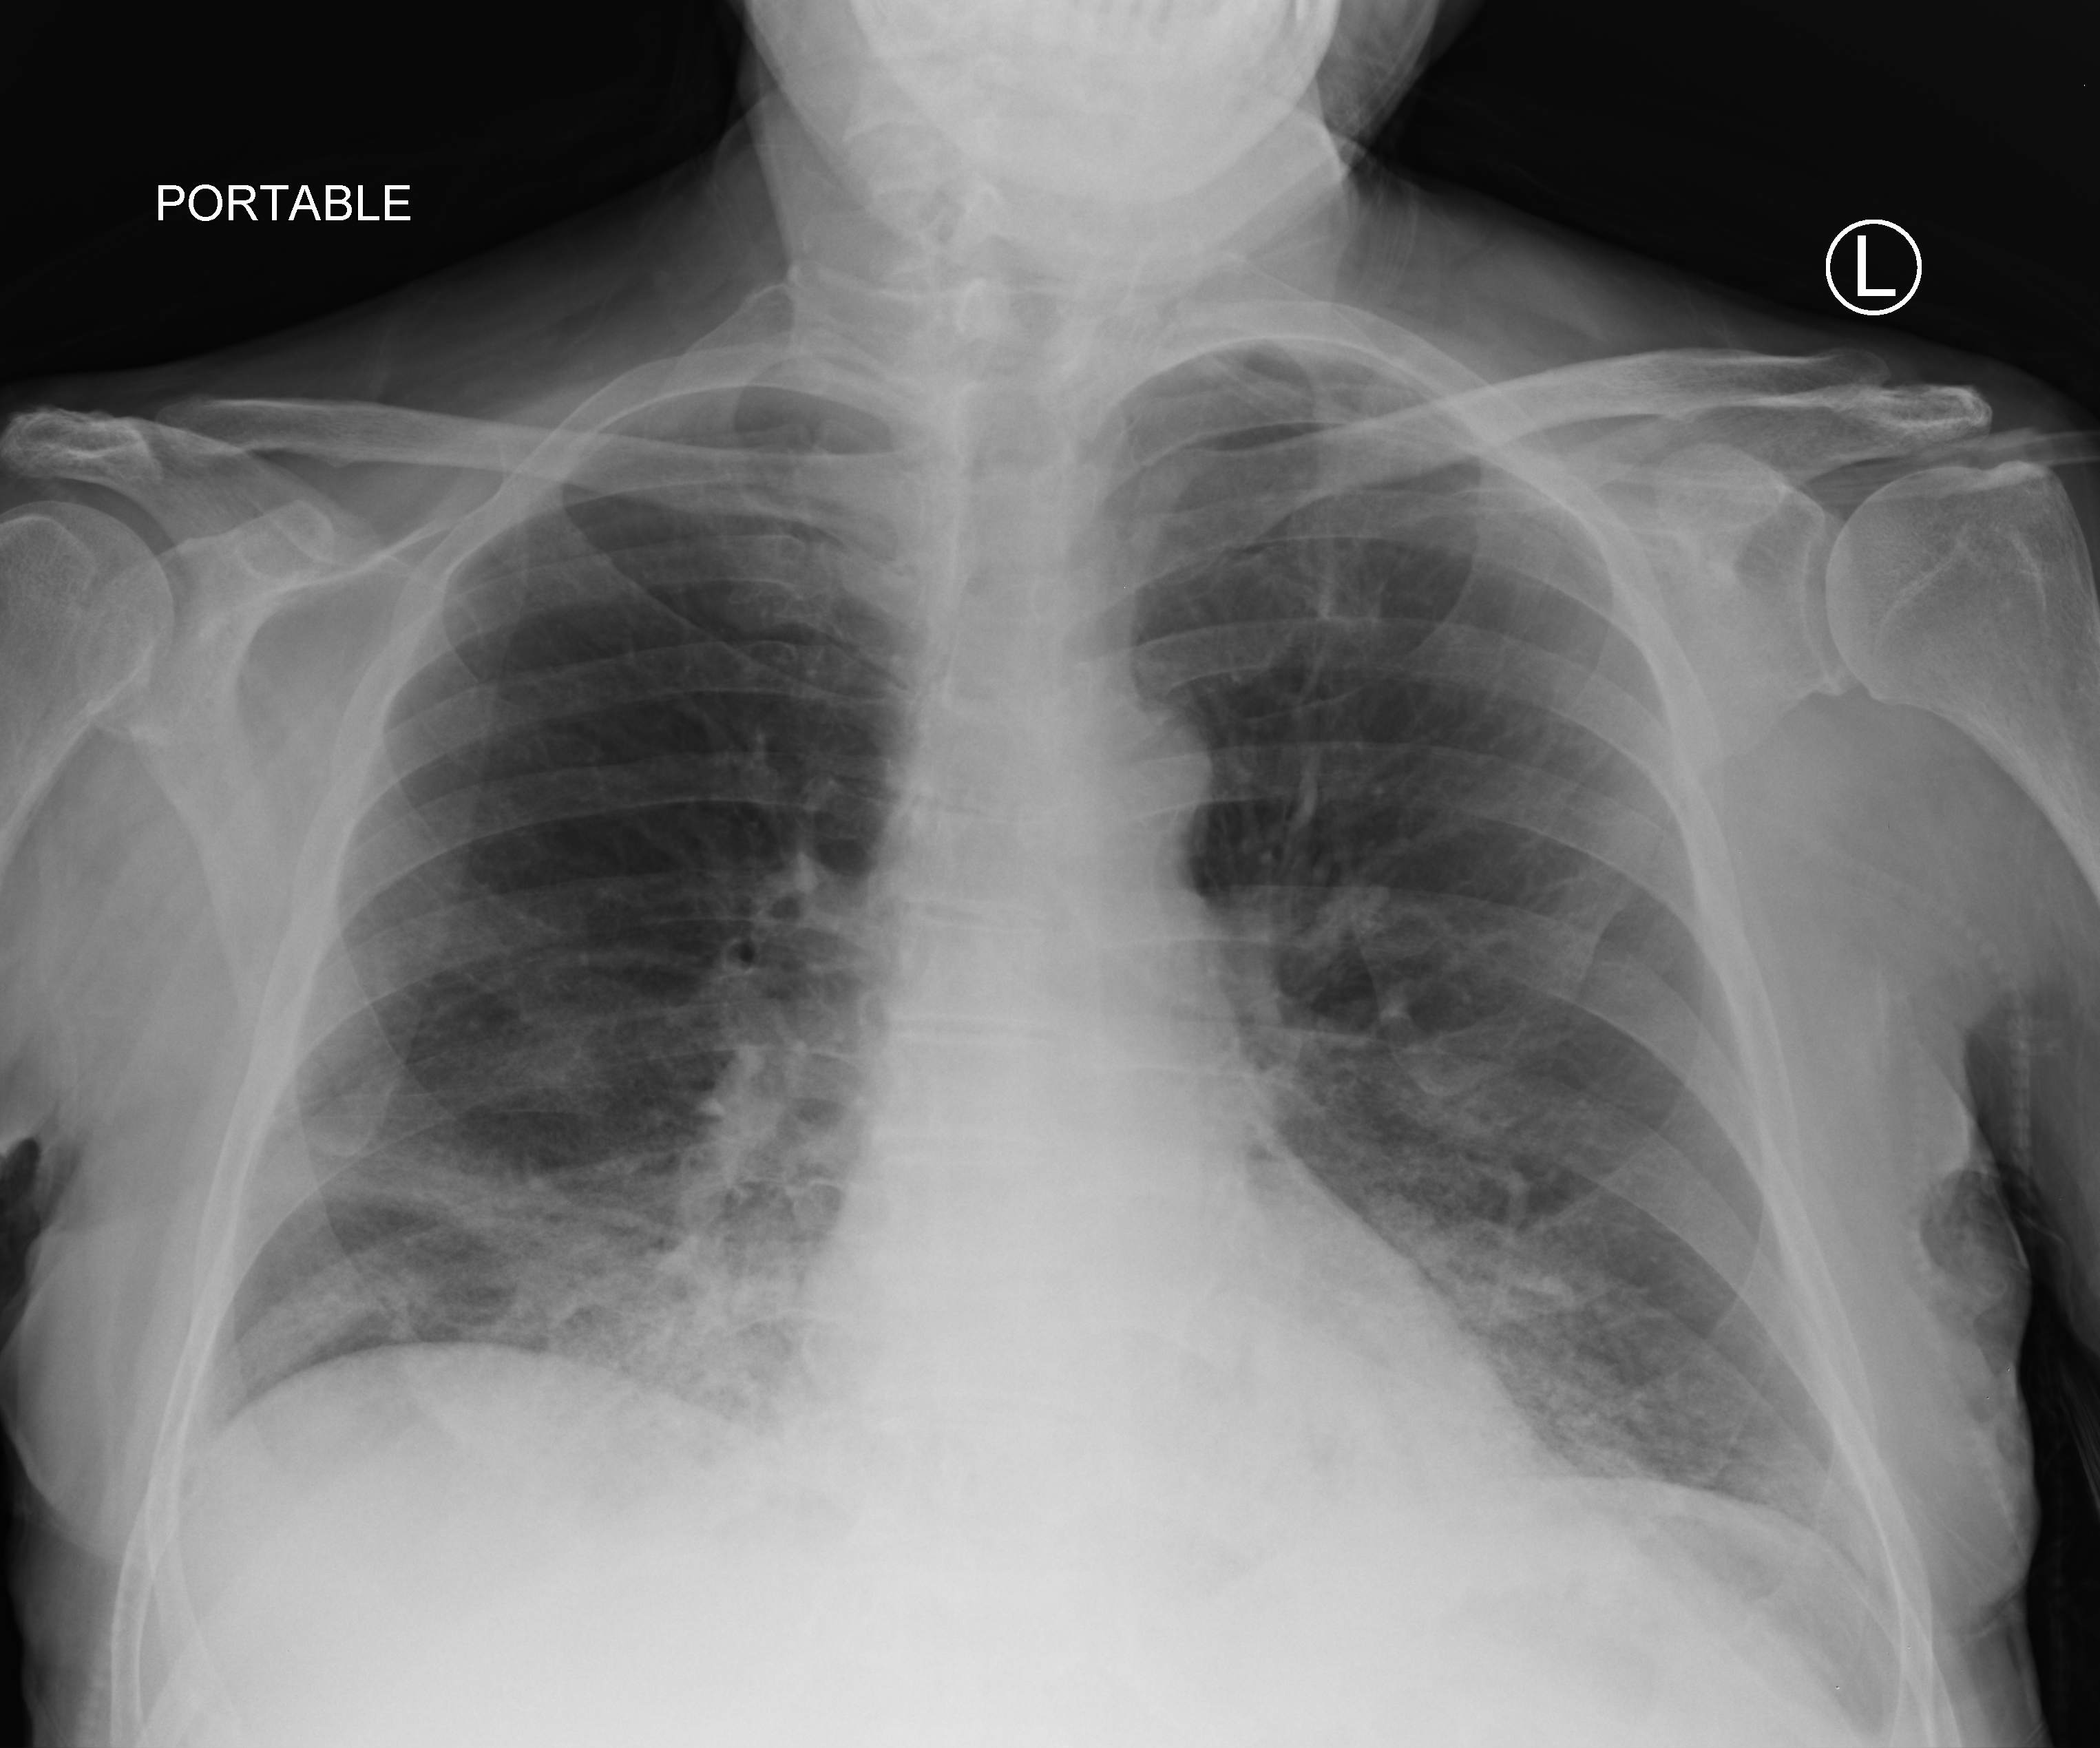
Portable chest radiograph, anteroposterior (AP) projection. Patient hospitalised with COVID-19; male, aged 60–74 years.
Admission-level facts for this patient (not findings on this image; timing relative to this image not recorded): length of hospital stay: 24 days.